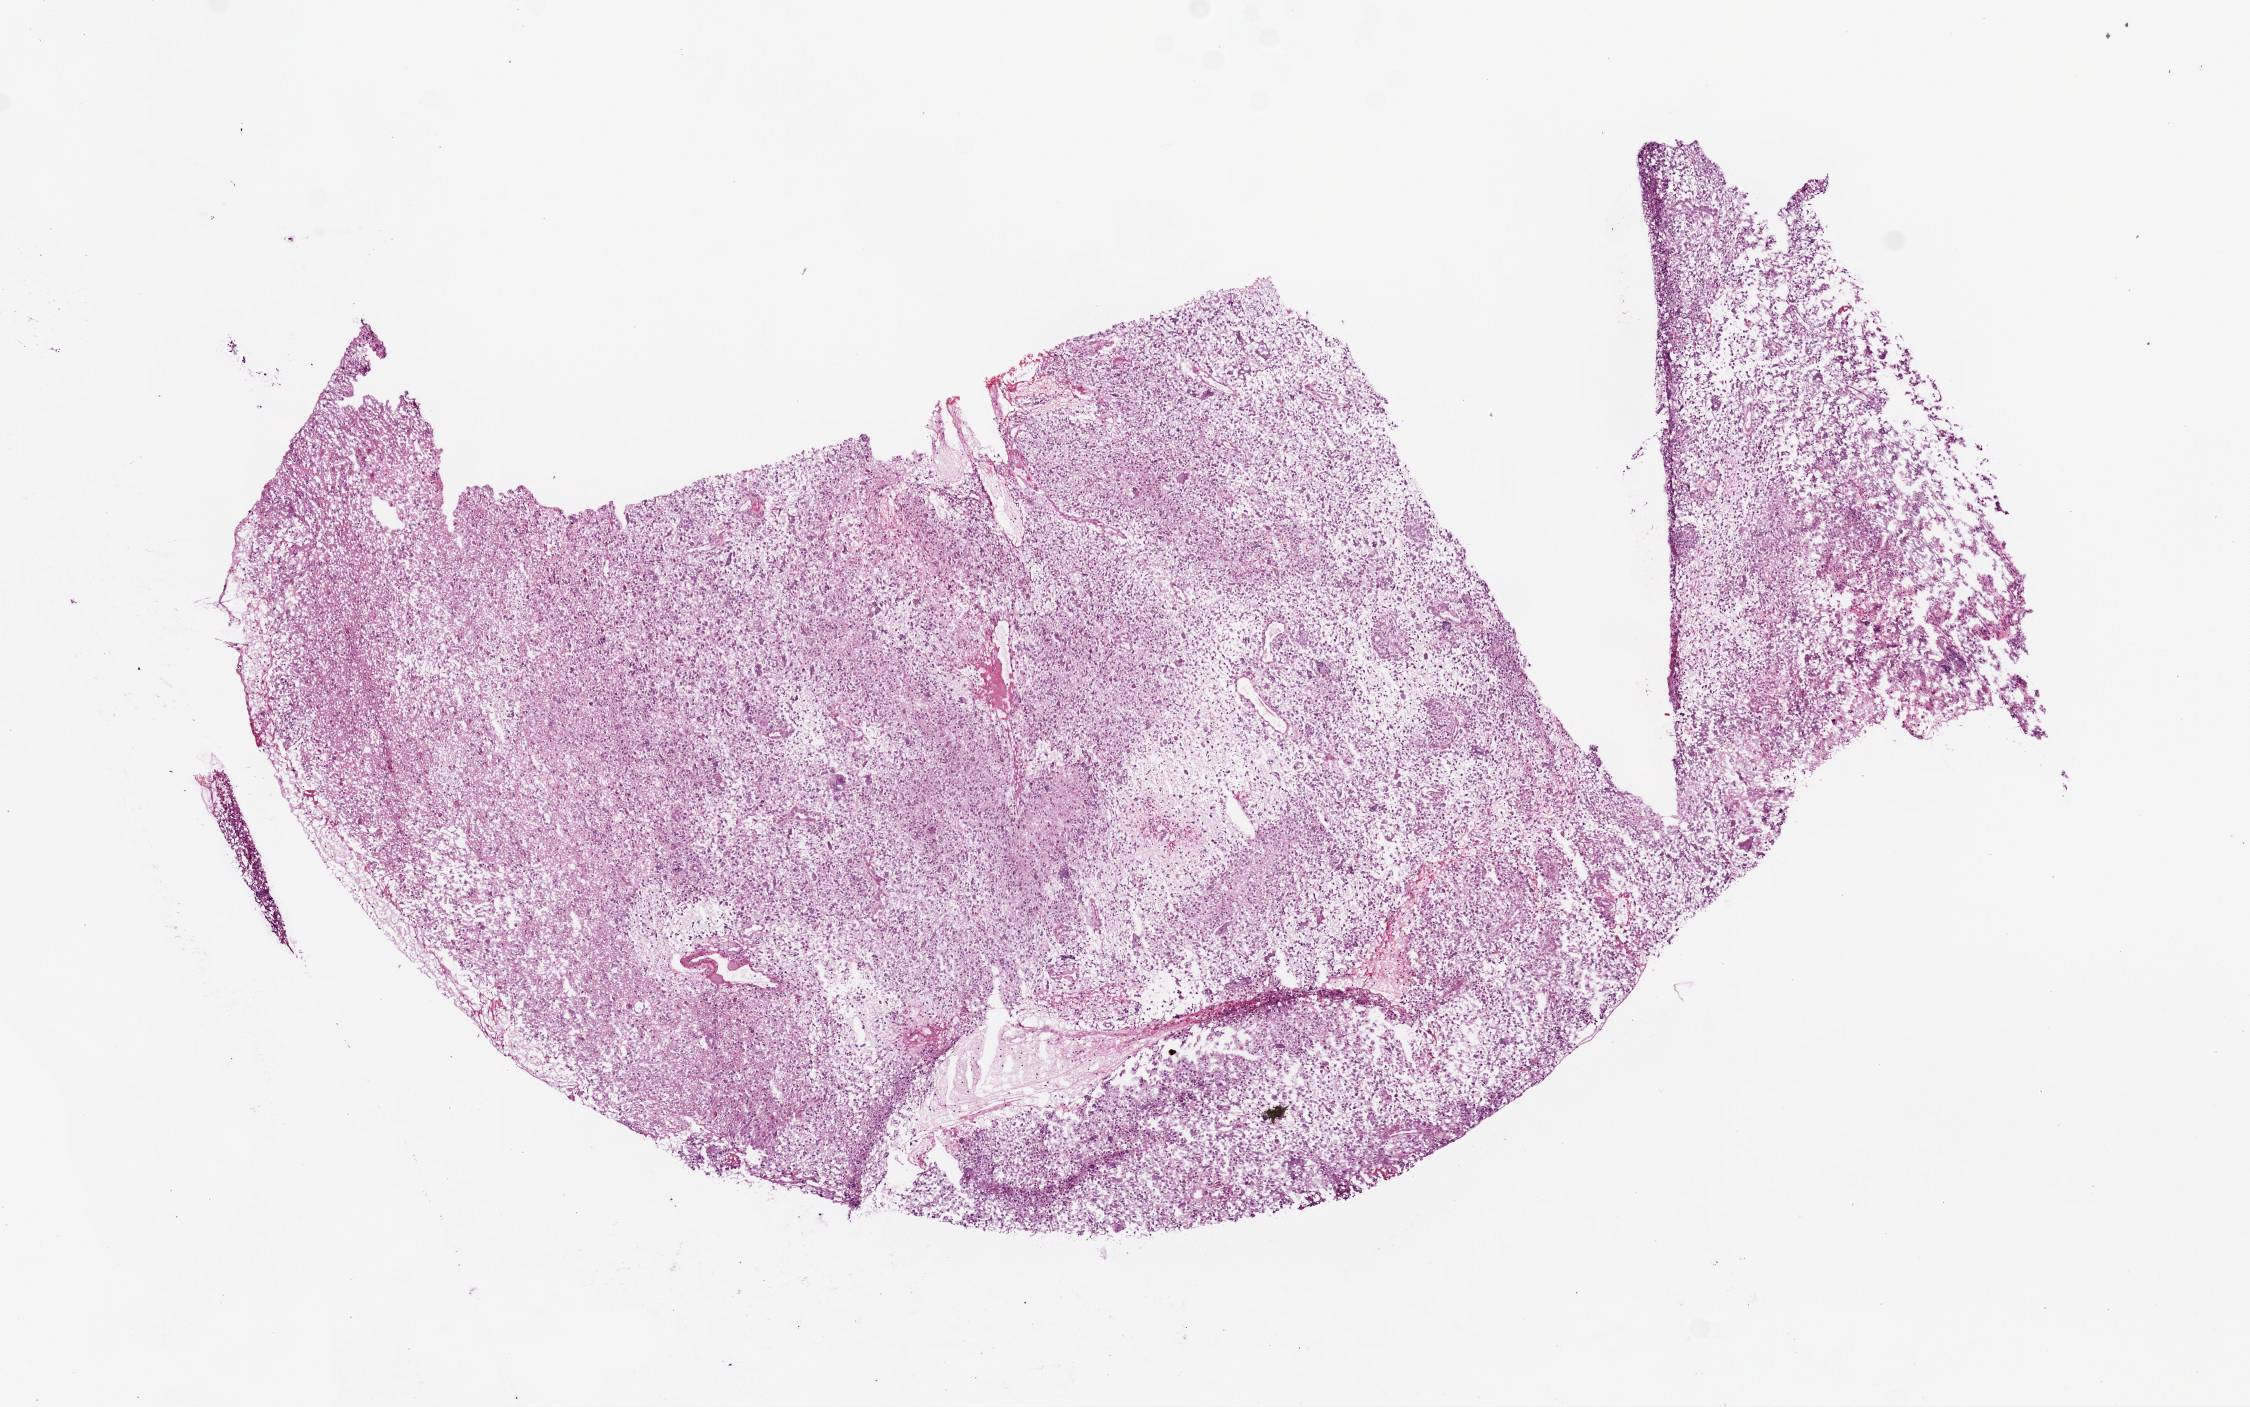
Digitized H&E tissue section (whole slide) — whole scanned area (about 9.0 x 5.6 mm, acquisition: 20x scan) shown as a low-resolution overview; frozen section; primary tumour sample from the brain. Female, age 48 years at initial diagnosis. Composition of this section per pathologist review: tumour cells 90%, tumour nuclei 85%, normal cells 0%, stromal cells 0%, necrosis 10%.
Diagnosis: Glioblastoma.